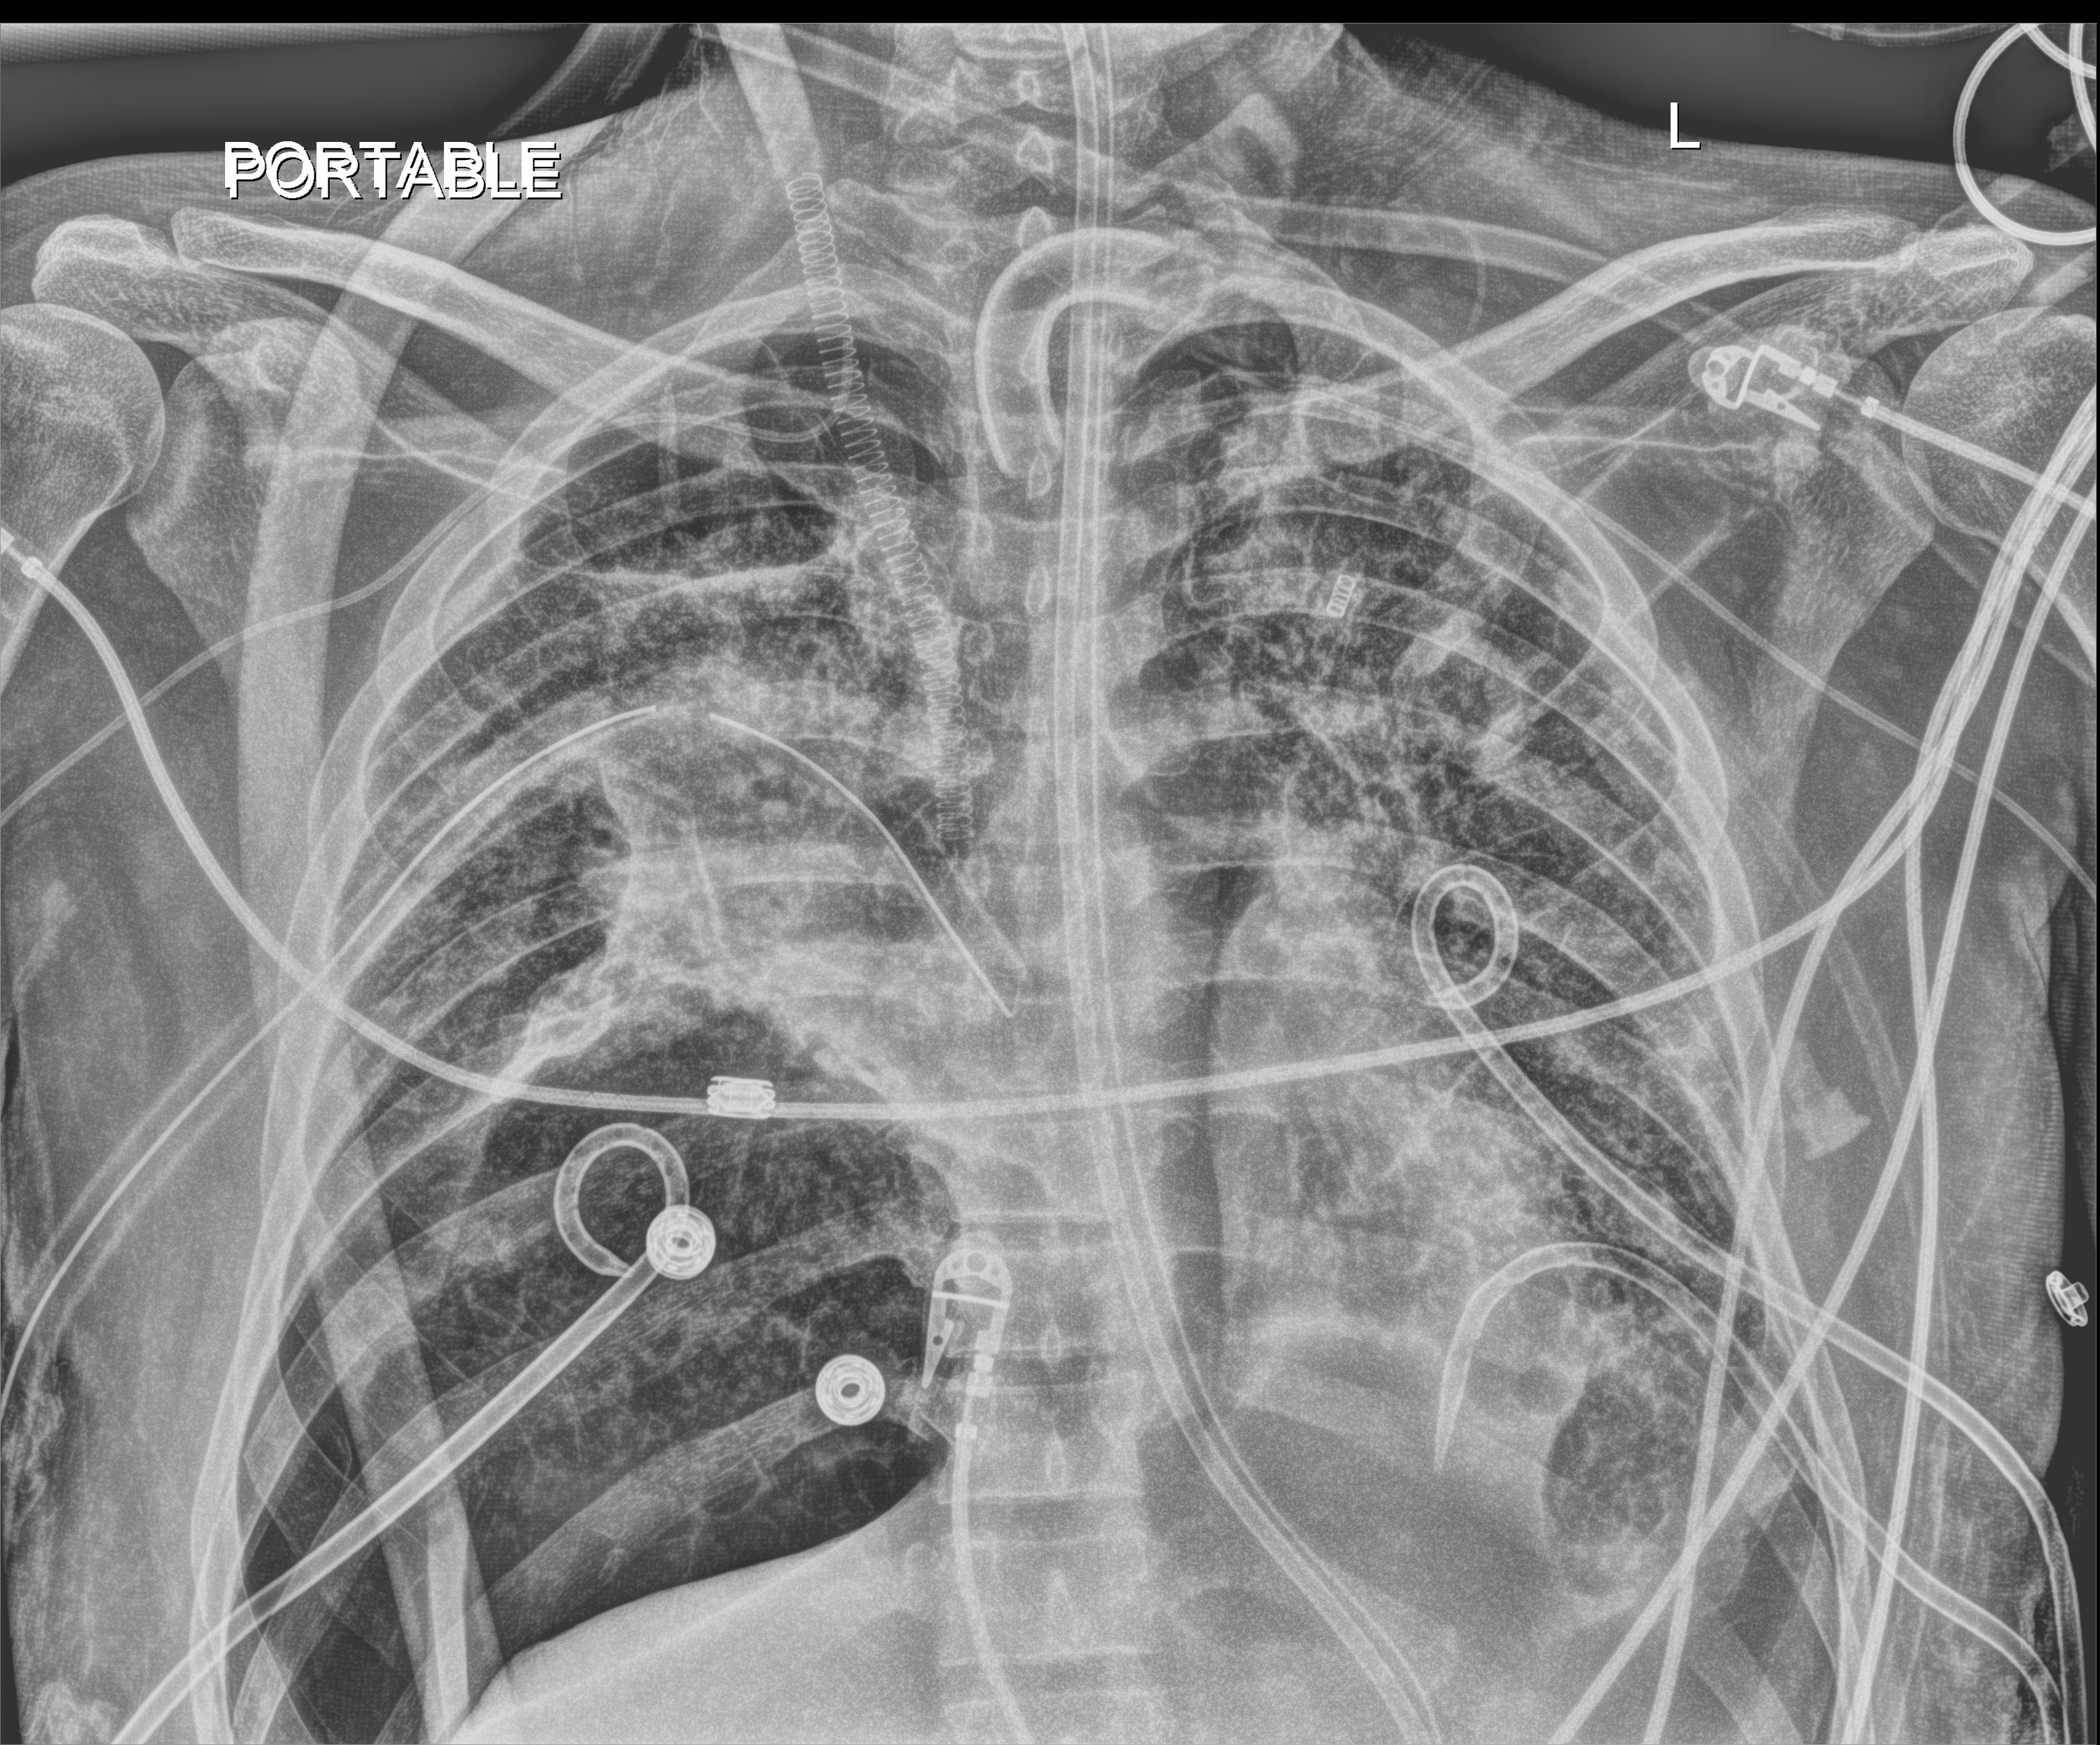
Chest X-ray (portable), anteroposterior (AP) projection. Patient hospitalised with COVID-19, aged 18–59 years.
From the hospital-stay record, not from the radiograph (when in the stay this image was taken is not recorded):
- length of hospital stay: 60 days
- admitted to intensive care during this hospital stay: yes
- COPD (admission record): no